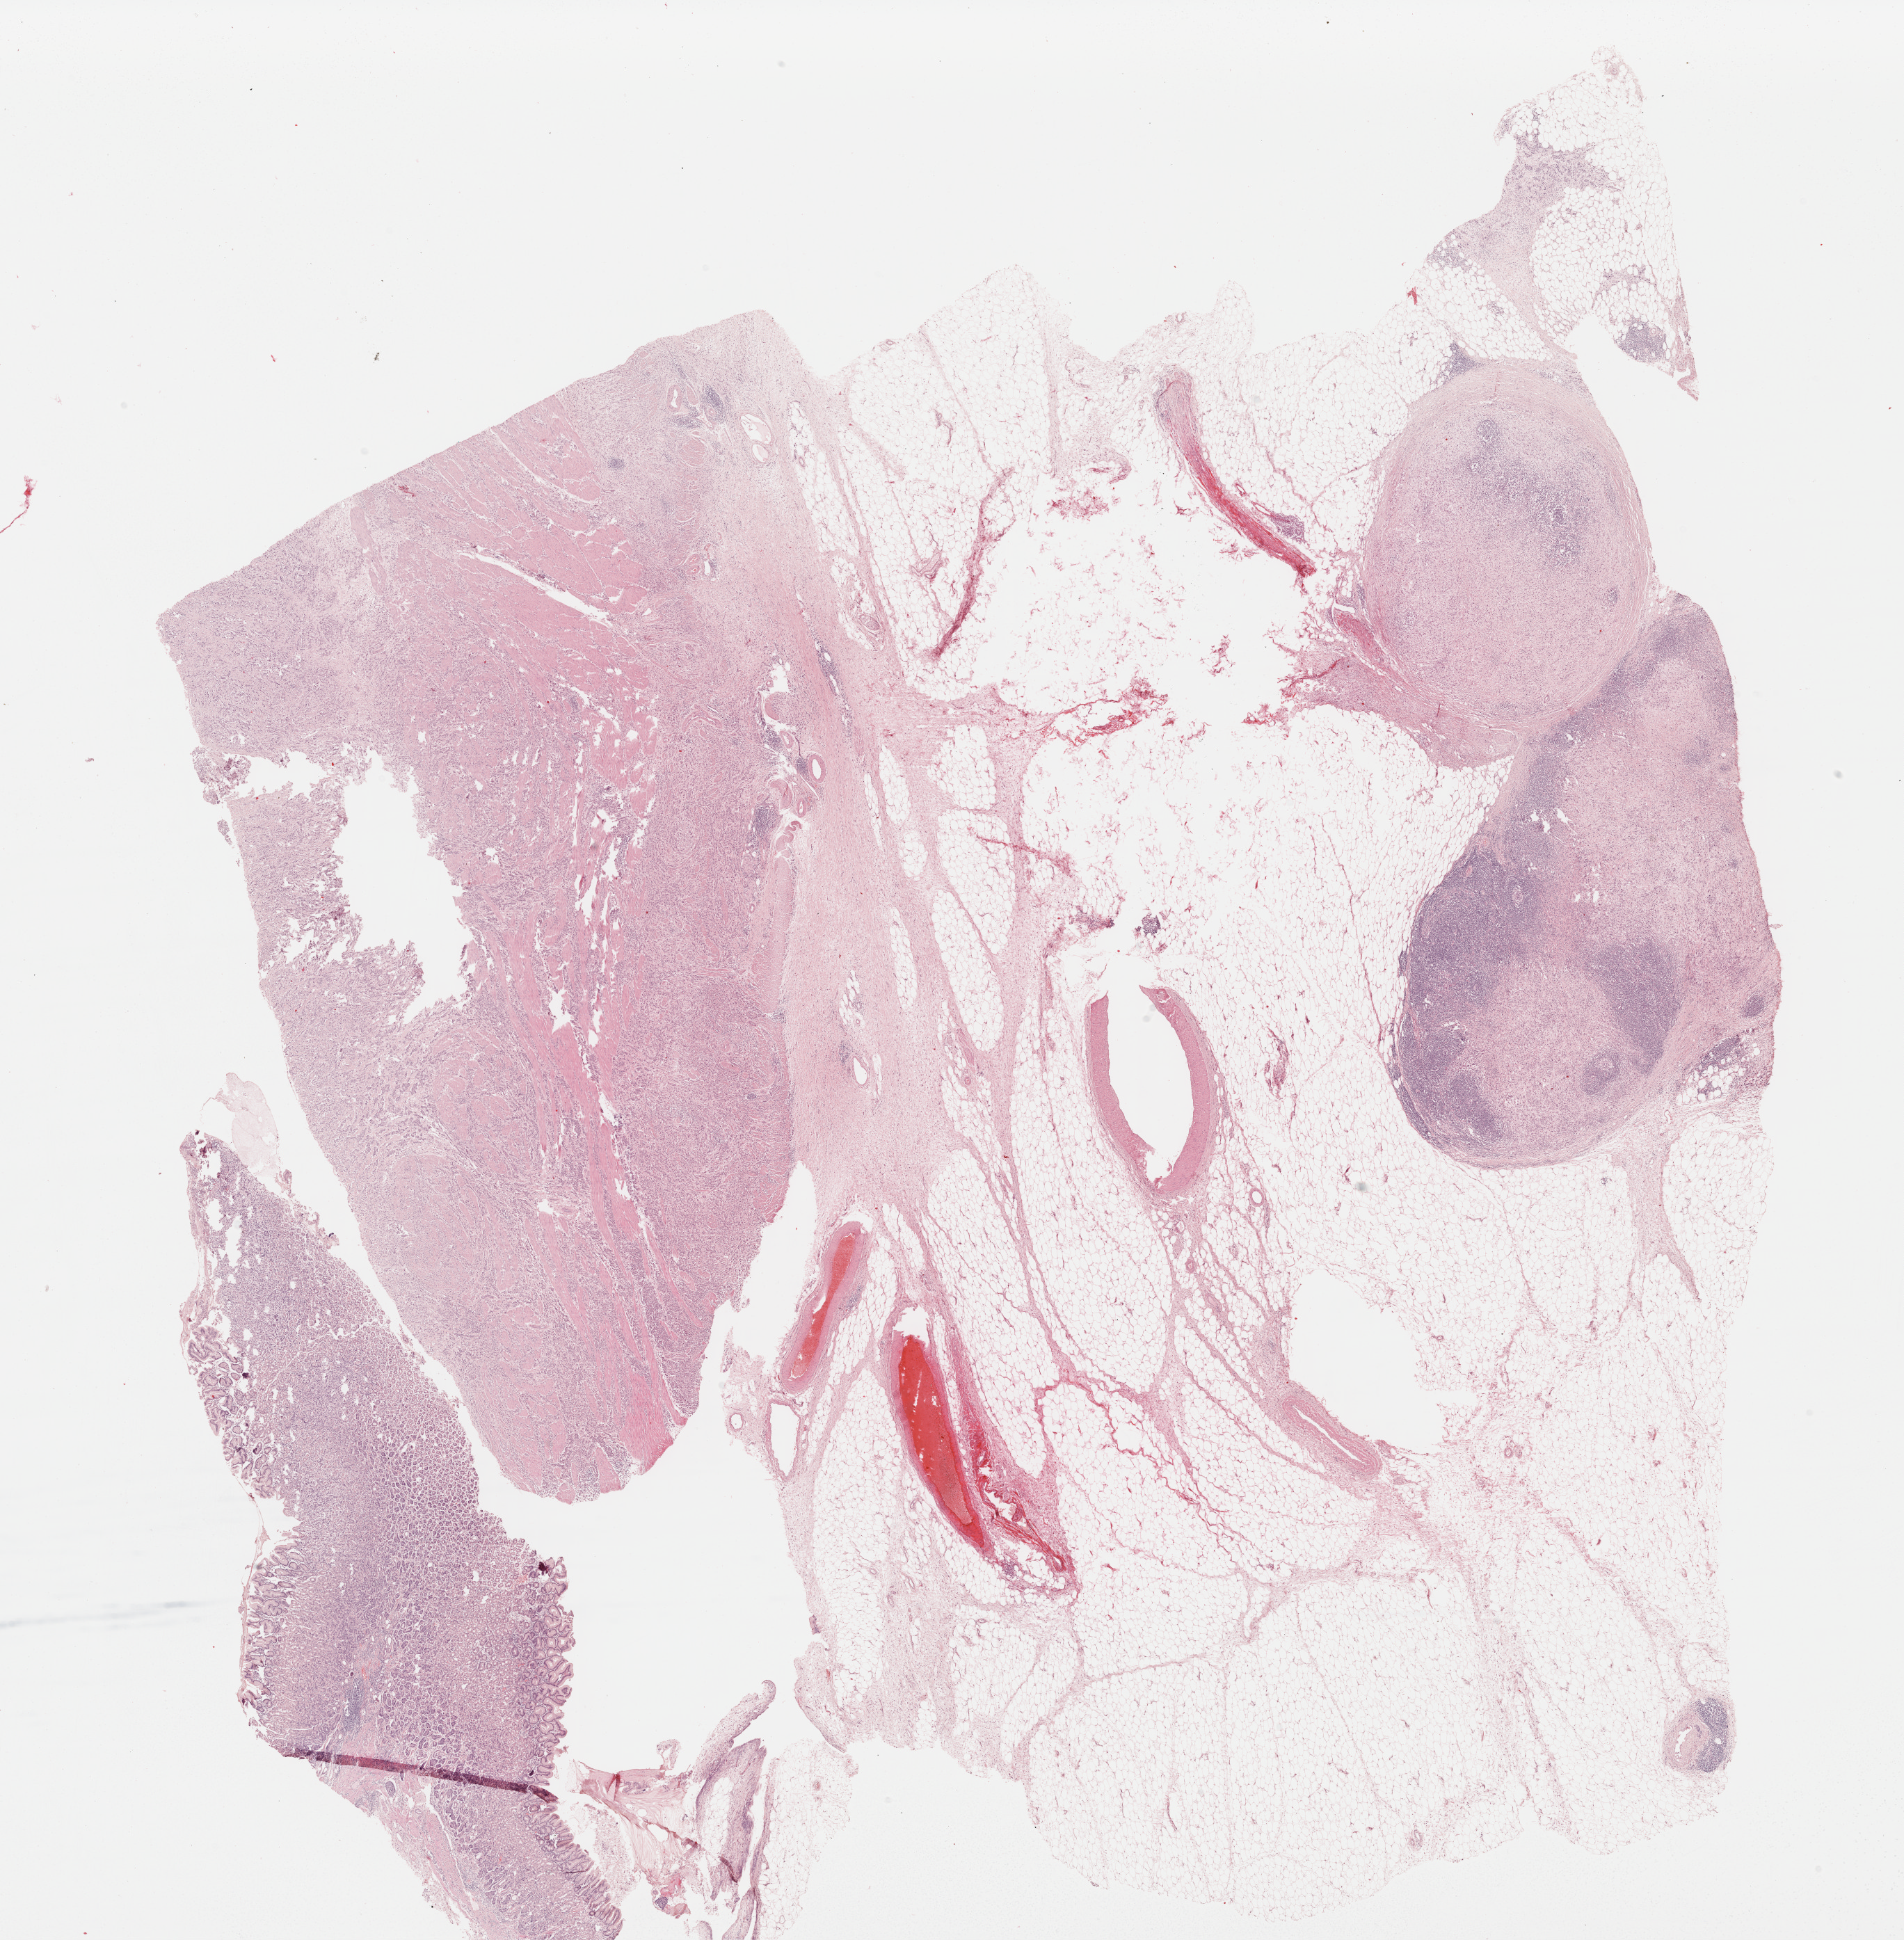
Whole-slide histology image, Hematoxylin and eosin (H&E) stained — low-resolution overview of the scanned area, about 21.5 x 21.9 mm (acquisition: 40x scan), formalin-fixed paraffin-embedded (FFPE) diagnostic section, stomach, primary tumour sample. Patient: male, age at initial diagnosis 65 years. Histologic grade: G3 (poorly differentiated).
Lymph nodes positive (case pathology): 15 of 17 examined. Diagnosis: Carcinoma, diffuse type (body of stomach).